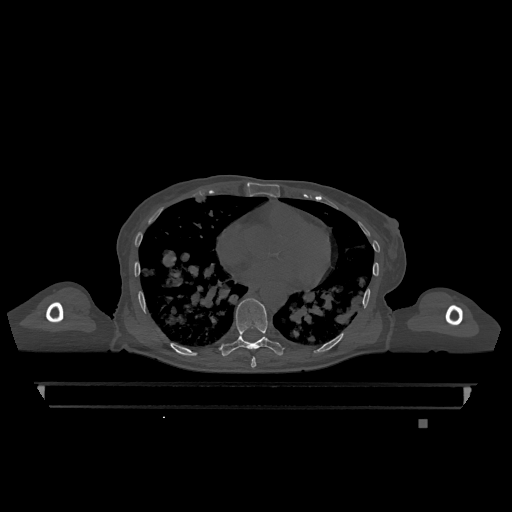
CT including the spine, one axial slice. Slice 694 of 1317 in the series (ordered by position). Bone window (W 1800 / L 400 HU). 512 × 512 image matrix. Female patient, age 74 years. From the clinical record (not read from this slice): primary cancer: lung; vertebrae with lytic lesions (as recorded): T1, T4, T5, T6, L4, L5.
Annotated regions visible in this slice (semi-automatically segmented with operator editing):
- T7 vertebra: bounding box <251,356,256,368> (left, top, right, bottom; pixels)
- T9 vertebra: <221,298,283,357>